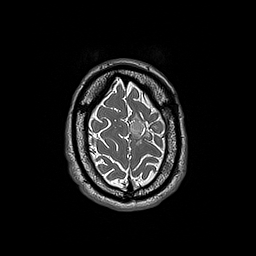
Brain MRI from a brain-tumour surgery series, one axial slice; position 41 of 192 along the scan axis; 1 mm slice thickness; 256 × 256 image matrix, field of view 250 × 250 mm. From the clinical record (not read from this slice): histopathology: Oligodendroglioma; WHO grade: 3; IDH mutation: yes; tumour location: Left Frontal.
Structures marked on this image (outlined manually by an expert reader):
- tumour: box from (x=130, y=117) to (x=157, y=145) px